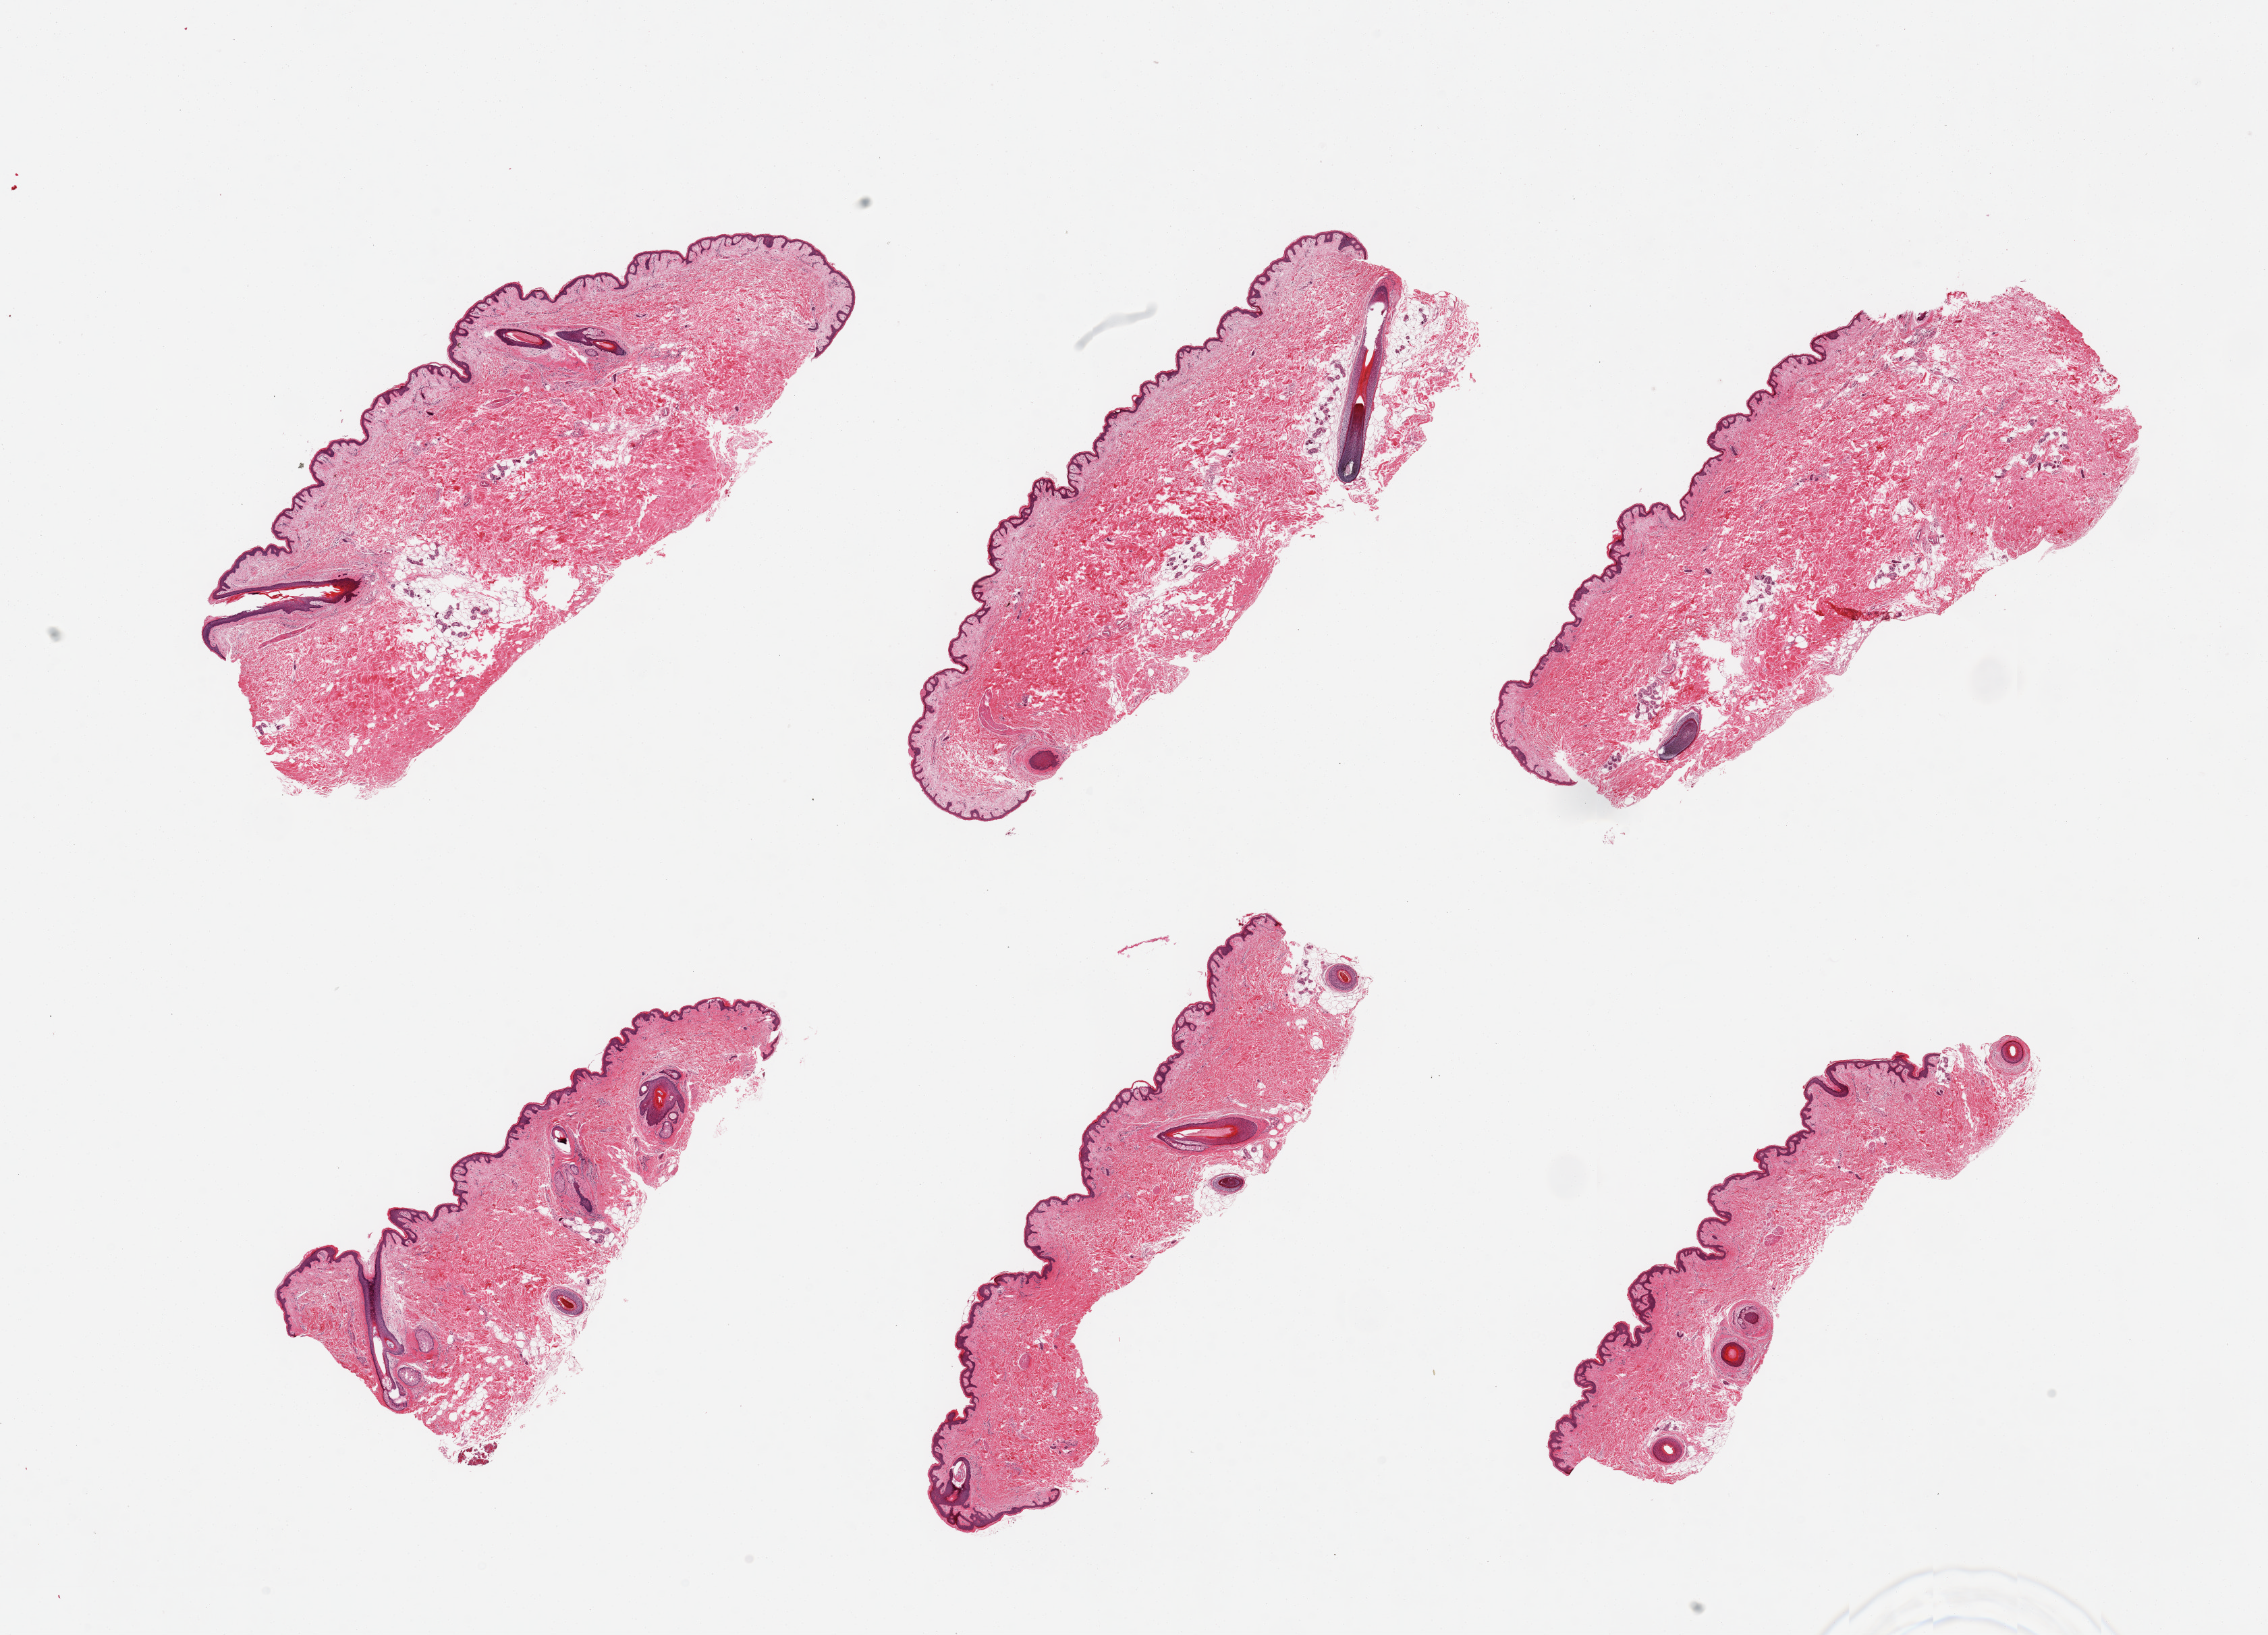
Whole-slide image, hematoxylin and eosin (H&E) stain, shown as a low-resolution overview of the whole scanned area (about 26.6 x 19.2 mm, acquisition: 20x scan); PAXgene-fixed paraffin-embedded (PFPE) section; sampled site (target tissue): skin of suprapubic region; donor tissue sample. Donor: female.
Pathologist's review note for this sample: 6 pieces; 2 to 4 hair follicles per piece; well trimmed.